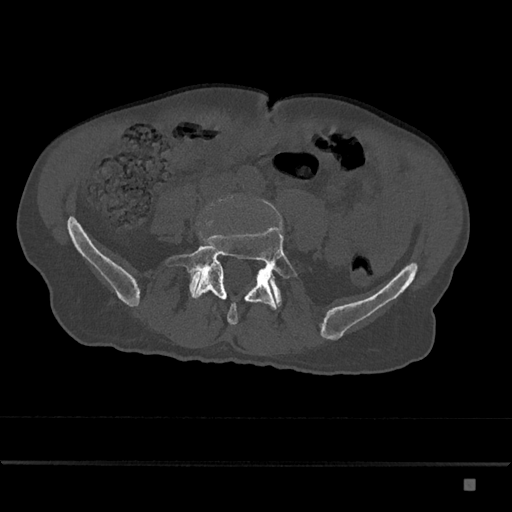
CT including the spine, one axial slice. Position 284 of 797 along the scan axis. Bone window (W 1800 / L 400 HU). 0.5 mm slice thickness. 512 × 512 image matrix. Male patient, age 72 years. Case-level facts recorded for this patient, not image findings: primary cancer: prostate.
Outlined on this slice (semi-automatically segmented with operator editing):
- L4 vertebra: box from (x=206, y=195) to (x=234, y=211) px
- L5 vertebra: (x=167, y=224)–(x=297, y=325)